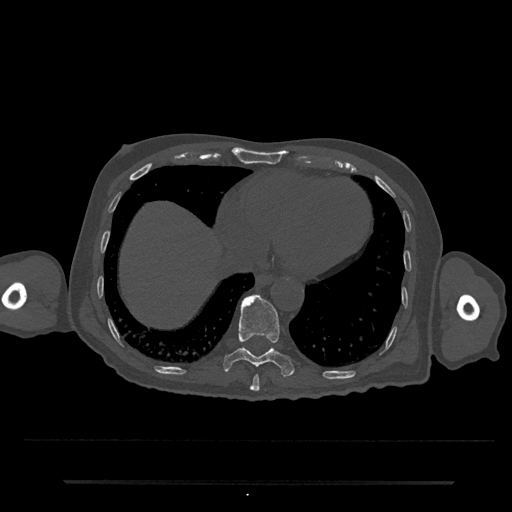
CT including the spine, one axial slice. Position 316 of 797 along the scan axis. Reconstruction kernel Br40s/3. 120 kVp. Bone window (W 1800 / L 400 HU). 0.5 mm slice thickness. 512 × 512 image matrix, field of view 427 × 427 mm. Patient: male, 74 years. Case-level facts recorded for this patient, not image findings: primary cancer: prostate.
Structures marked on this image (semi-automatically segmented with operator editing):
- T10 vertebra: bounding box (x1, y1, x2, y2) in pixels: (223, 294, 294, 377)
- T9 vertebra: (250, 374, 260, 392)